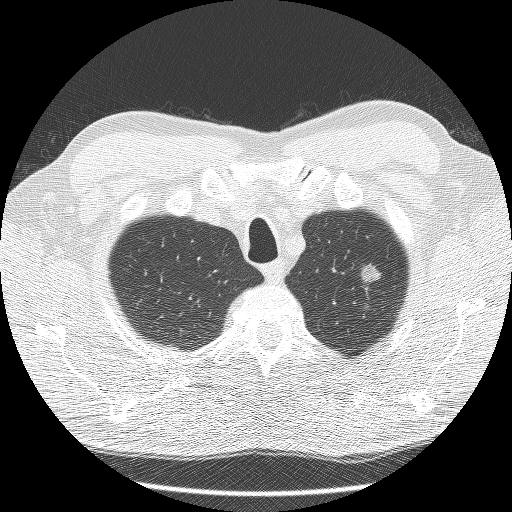
Axial slice from a low-dose chest CT screening exam, third screening round (two years after baseline), lung window (W 1500 / L -600 HU), lung (sharp) reconstruction kernel (BONE), slice 15 of 132 in the series, 512 × 512 image matrix, field of view 340 × 340 mm. Male participant, aged 60 years at enrolment. Former smoker at enrolment.
Lesion marked by an expert reader, bounding box (x1, y1, x2, y2) in pixels: (336, 253, 393, 300). The screening reader recorded 2 non-calcified nodules or masses ≥4 mm on this exam (right lower lobe, left upper lobe); which of them this box marks is not recorded. Lung cancer was diagnosed 99 days after this screen: bronchiolo-alveolar carcinoma, non-mucinous, left upper lobe, well differentiated (G1), stage IA (AJCC 6th edition), 16 mm at pathology.